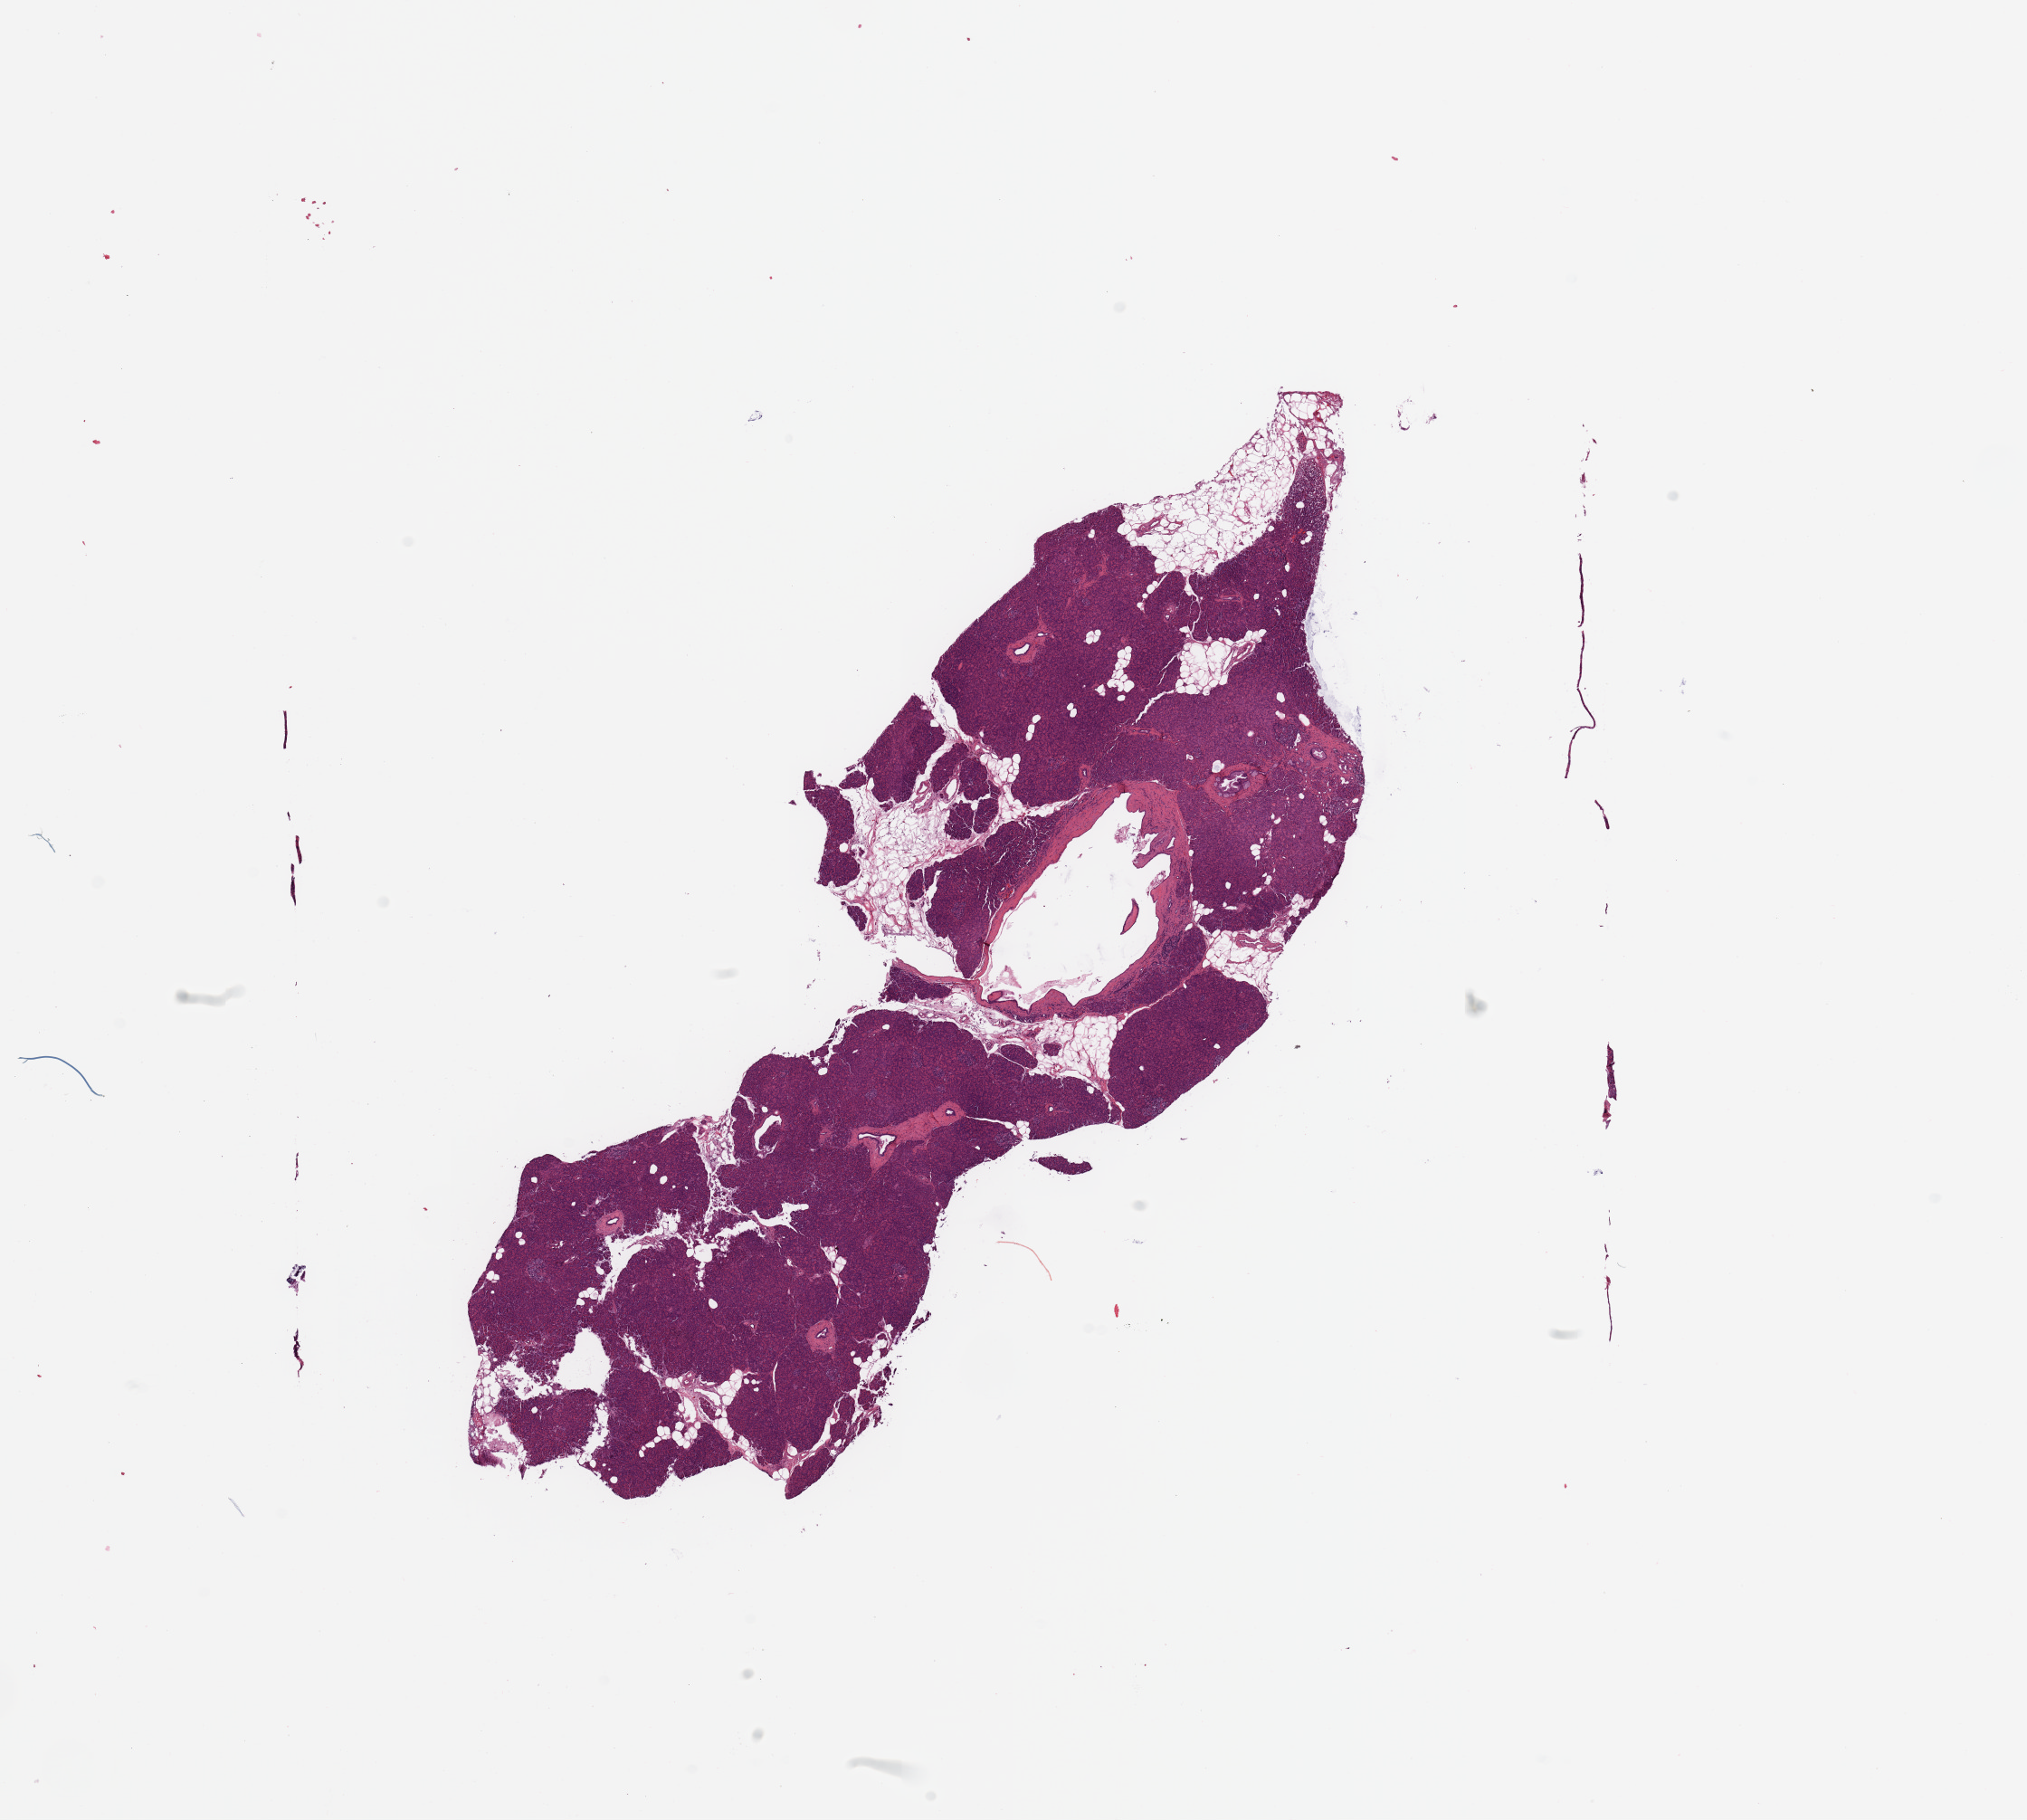
Digitized H&E tissue section (whole slide), low-resolution overview of the scanned area, about 17.7 x 15.9 mm, normal (non-tumour) tissue sample, pancreas. Patient: male, age 80 years.
* this section: normal (non-tumour) tissue from the same patient
* patient diagnosis: Infiltrating duct carcinoma, NOS